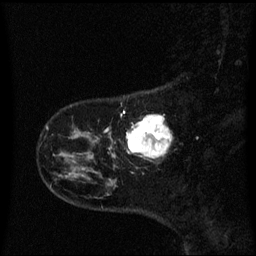
Breast MRI (dynamic contrast-enhanced), one sagittal slice; slice 11 of 60 in the series (ordered by position); dynamic contrast-enhanced series, image 2 of 3 at this slice position (ordered by acquisition); 1.5 T; TE 4.2 ms, TR 8.4 ms; 256 × 256 image matrix. Female patient, age 41 years. Case-level facts recorded for this patient, not image findings: setting: breast cancer imaged before/during neoadjuvant chemotherapy; receptor status: triple-negative.
Outlined on this slice (semi-automatically segmented with operator editing):
- analysis volume of interest (the breast-tissue region the enhancement analysis was run in; not a lesion): bounding box [x1, y1, x2, y2] px = [127, 116, 171, 159]
- tumour enhancement mask (voxels above the 70 % enhancement threshold inside the analysis volume of interest): [127, 116, 171, 159]